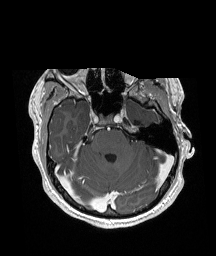
Brain MRI from a brain-tumour surgery series, one axial slice. Position 124 of 192 along the scan axis. T1-weighted post-contrast. 216 × 256 image matrix. Case-level facts recorded for this patient, not image findings: histopathology: Glioneuronal tumor; WHO grade: 2; tumour location: Left Superior Temporal Gyrus.
Outlined on this slice (outlined manually by an expert reader):
- previous resection cavity: bounding box (x1, y1, x2, y2) in pixels: (135, 121, 140, 125)